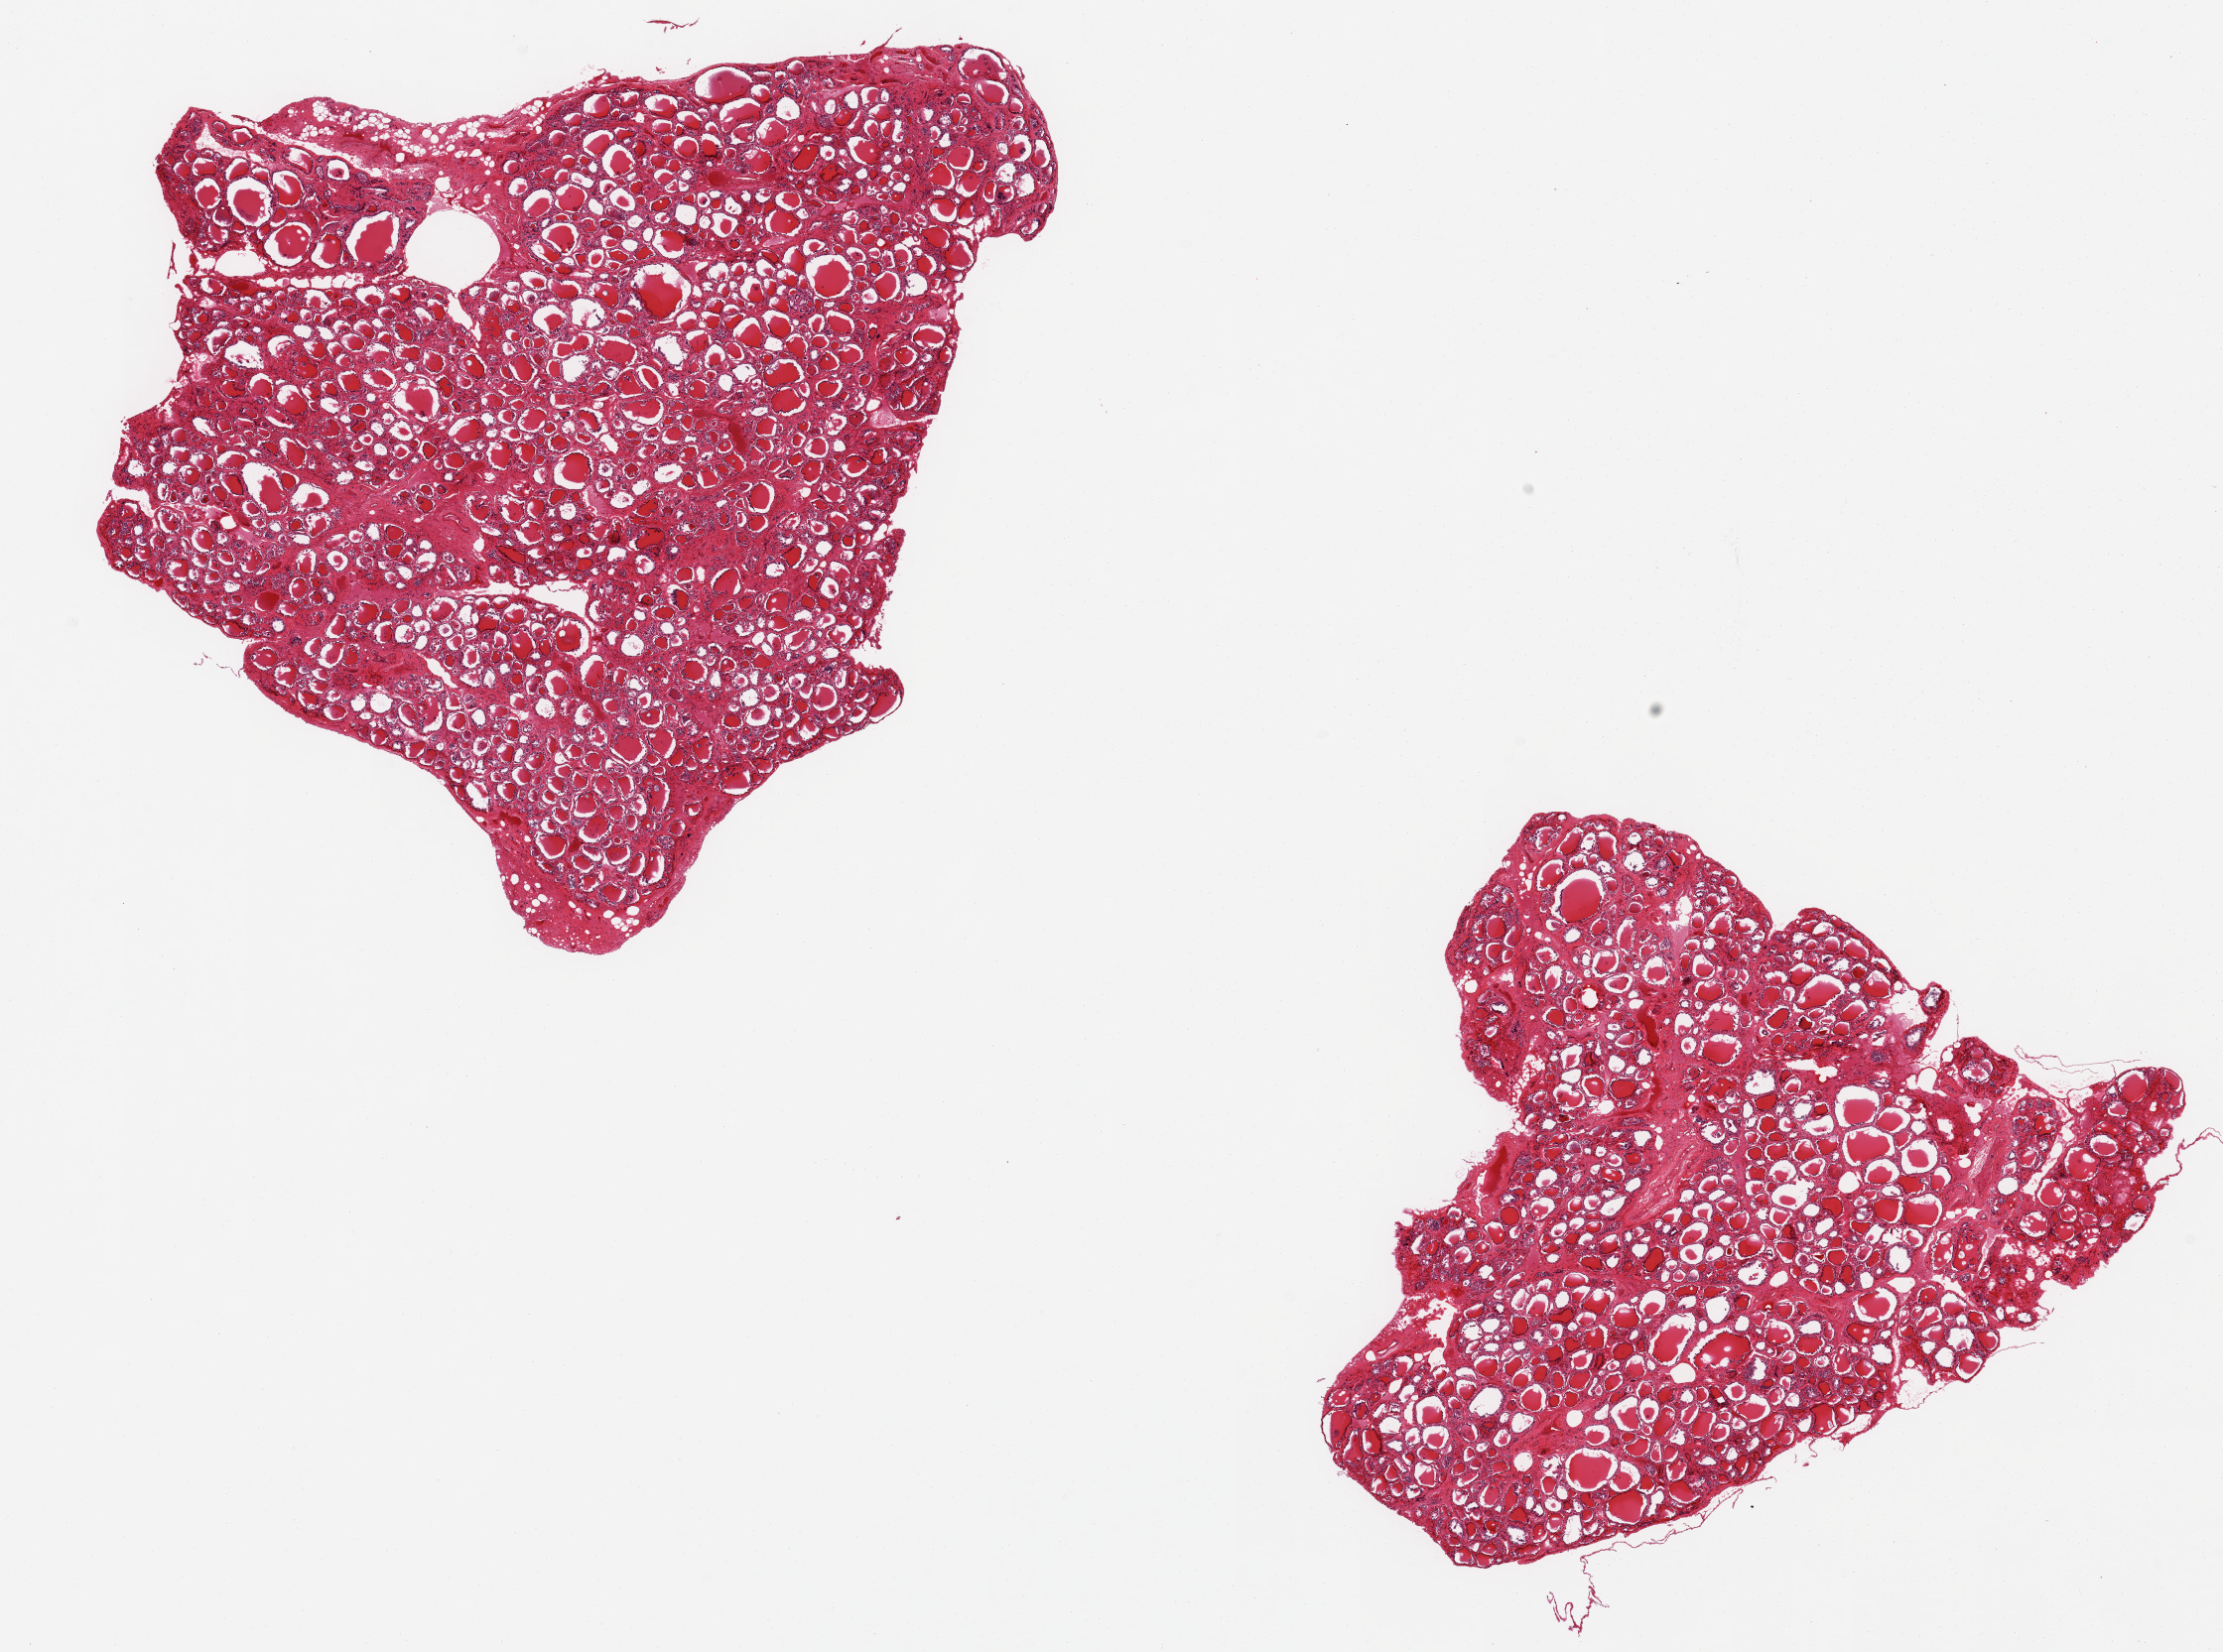
H&E whole-slide image, shown as a low-resolution overview of the whole scanned area (about 17.7 x 13.2 mm, acquisition: 20x scan); PAXgene-fixed paraffin-embedded (PFPE) section; section of thyroid (target tissue); tissue donor sample. Male donor.
Reviewer comment on this tissue sample: 2 aliquots, ~8x6mm.